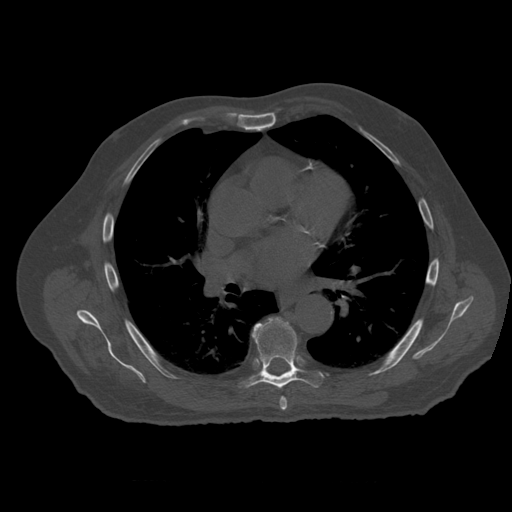
CT including the spine, one axial slice; slice 365 of 399 in the series (ordered by position); reconstruction kernel STANDARD; 120 kVp; bone window (W 1800 / L 400 HU); 1.25 mm slice thickness; 512 × 512 image matrix, field of view 407 × 407 mm. Patient age 73 years. From the clinical record (not read from this slice): primary cancer: prostate; vertebrae with lytic lesions (as recorded): L2.
Annotated regions visible in this slice (semi-automatically segmented with operator editing):
- T6 vertebra: bounding box [x1, y1, x2, y2] px = [280, 397, 288, 411]
- T7 vertebra: [246, 319, 325, 389]